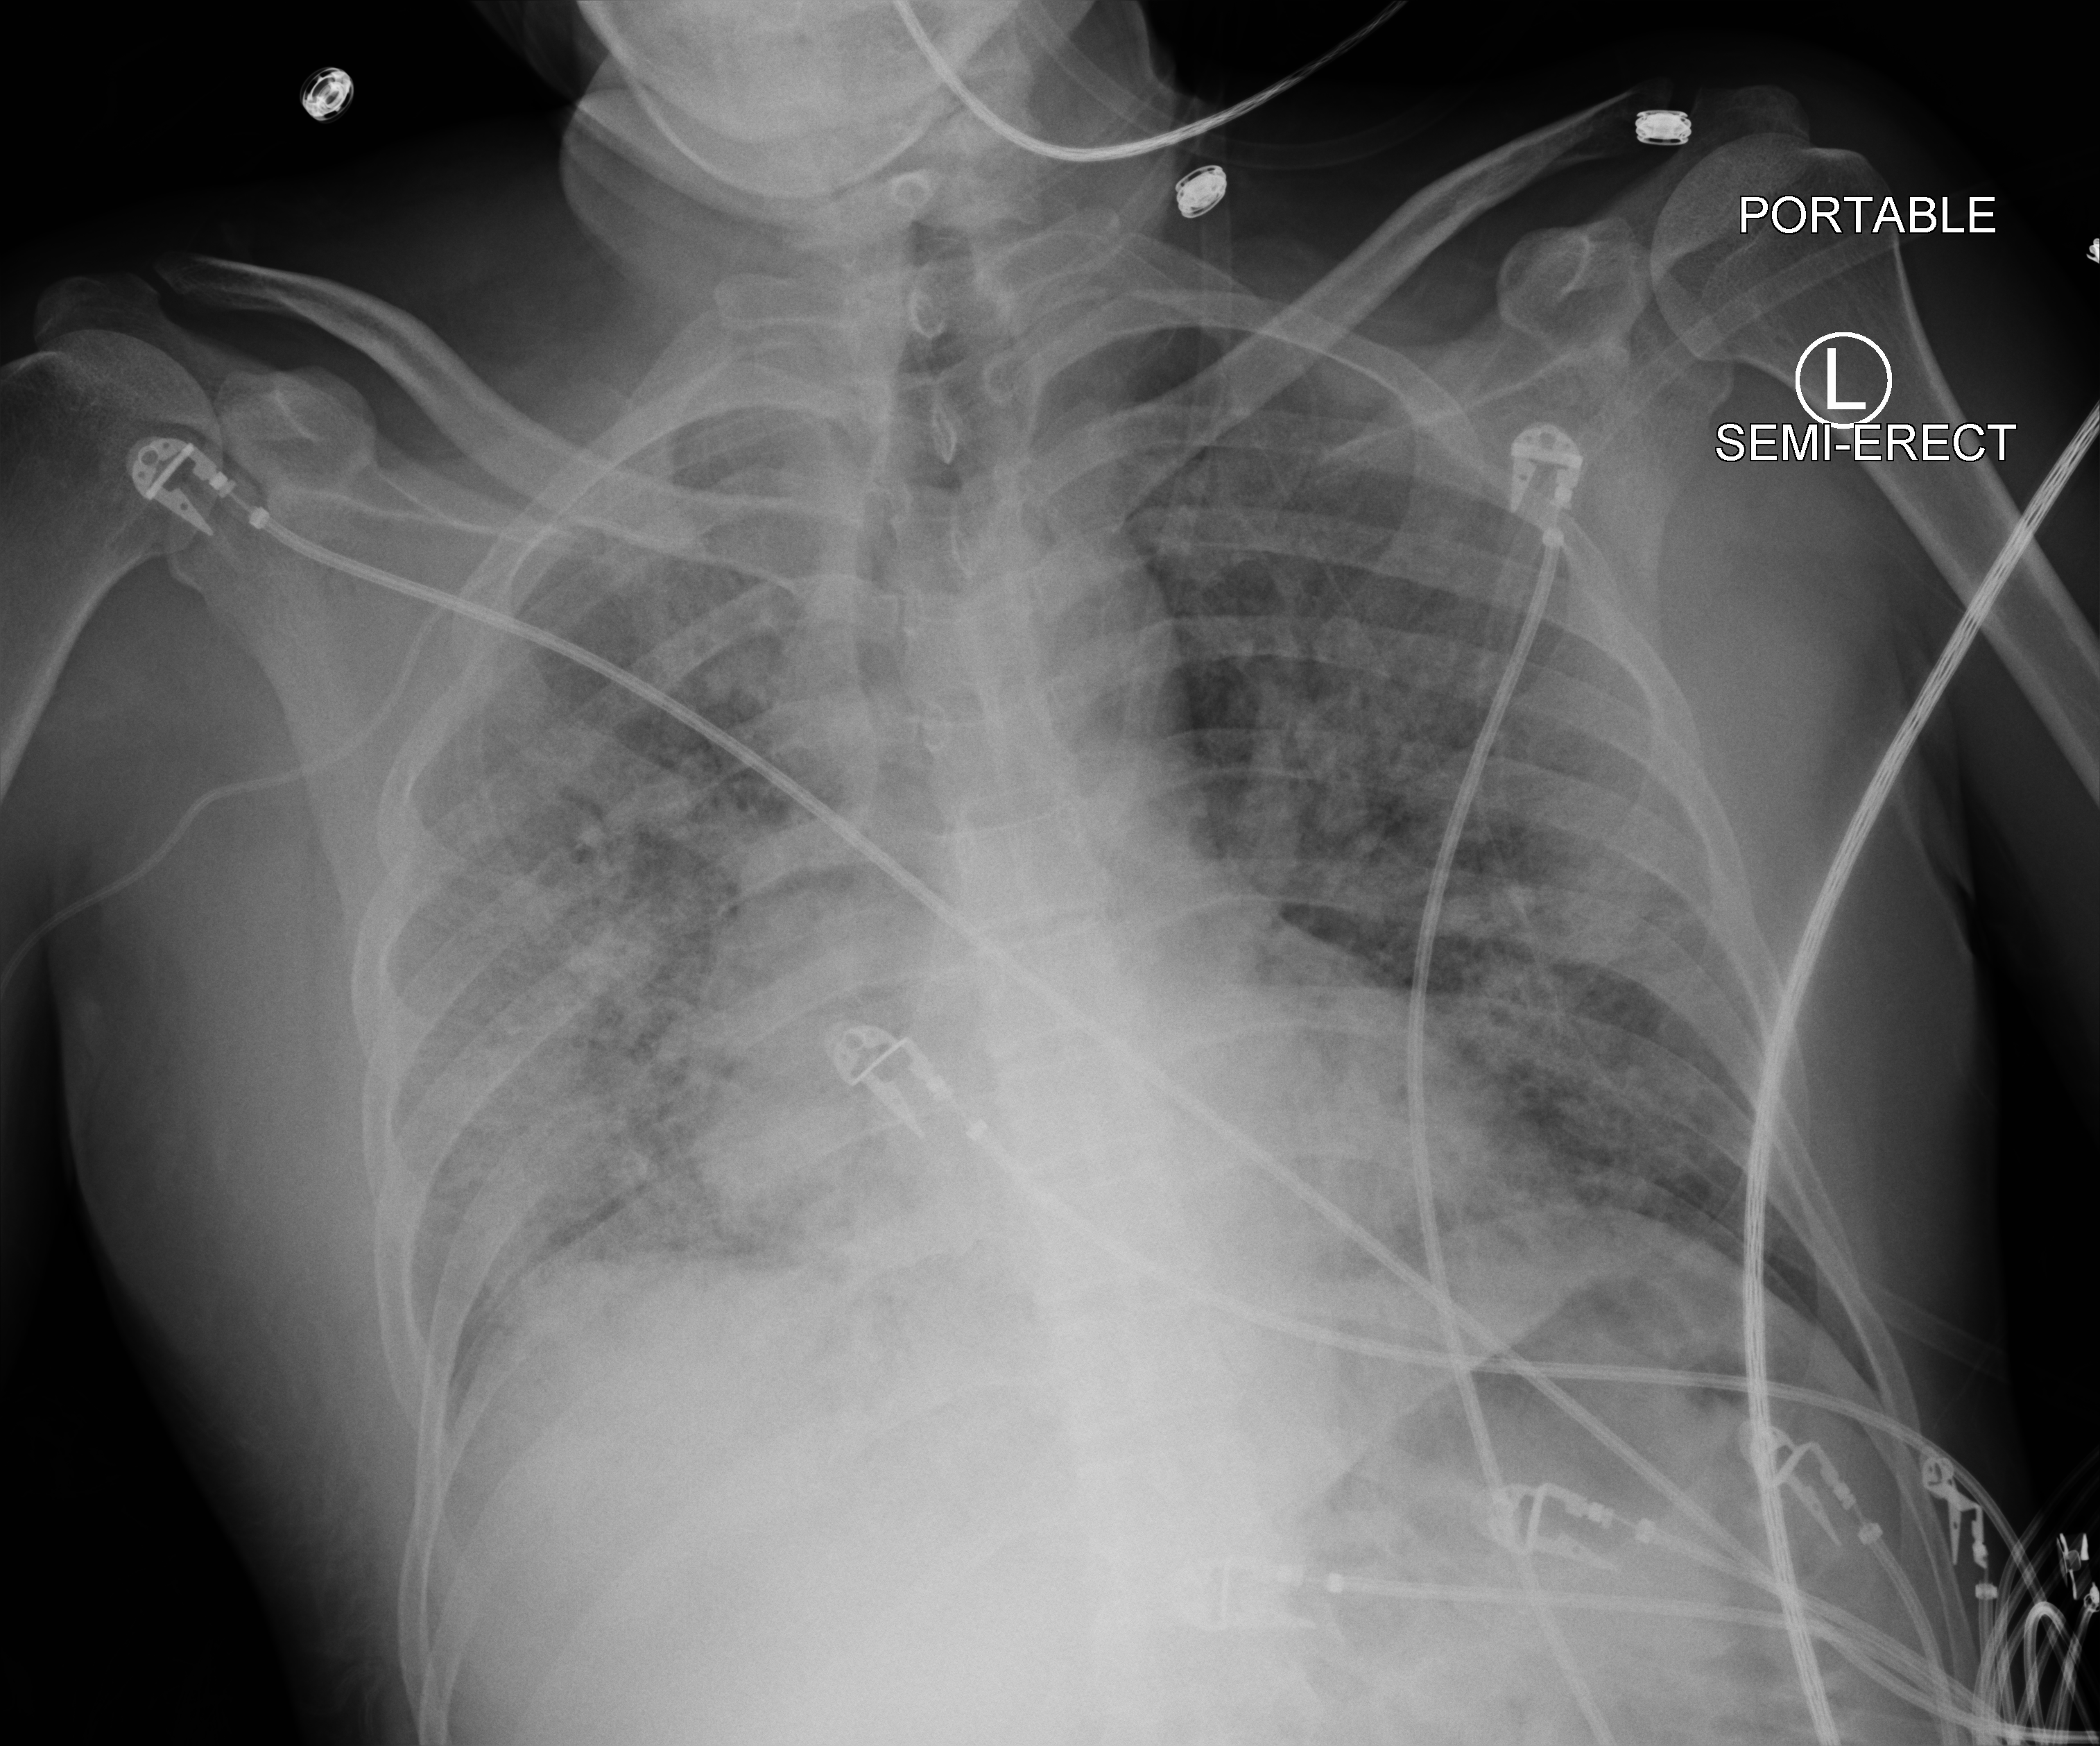
Chest X-ray (portable); anteroposterior (AP) projection. Adult patient hospitalised with COVID-19, age 18–59 years.
Admission-level facts for this patient (not findings on this image; timing relative to this image not recorded):
- admitted to intensive care during this hospital stay: yes